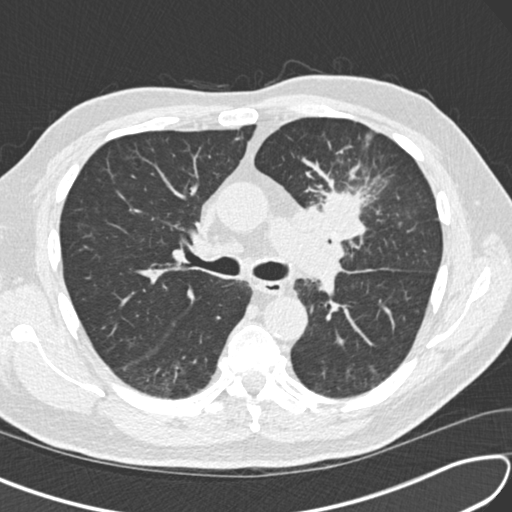
Low-dose screening chest CT, one axial slice; slice 97 of 156 in the series (ordered by position); reconstruction kernel B30f; 120 kVp; lung window (W 1500 / L -600 HU); 2 mm slice thickness; 512 × 512 image matrix, field of view 340 × 340 mm.
Outlined on this slice (manually delineated by an expert):
- lesion 1 (tumor, upper lobe of left lung): bounding box [x1, y1, x2, y2] px = [319, 190, 365, 239]